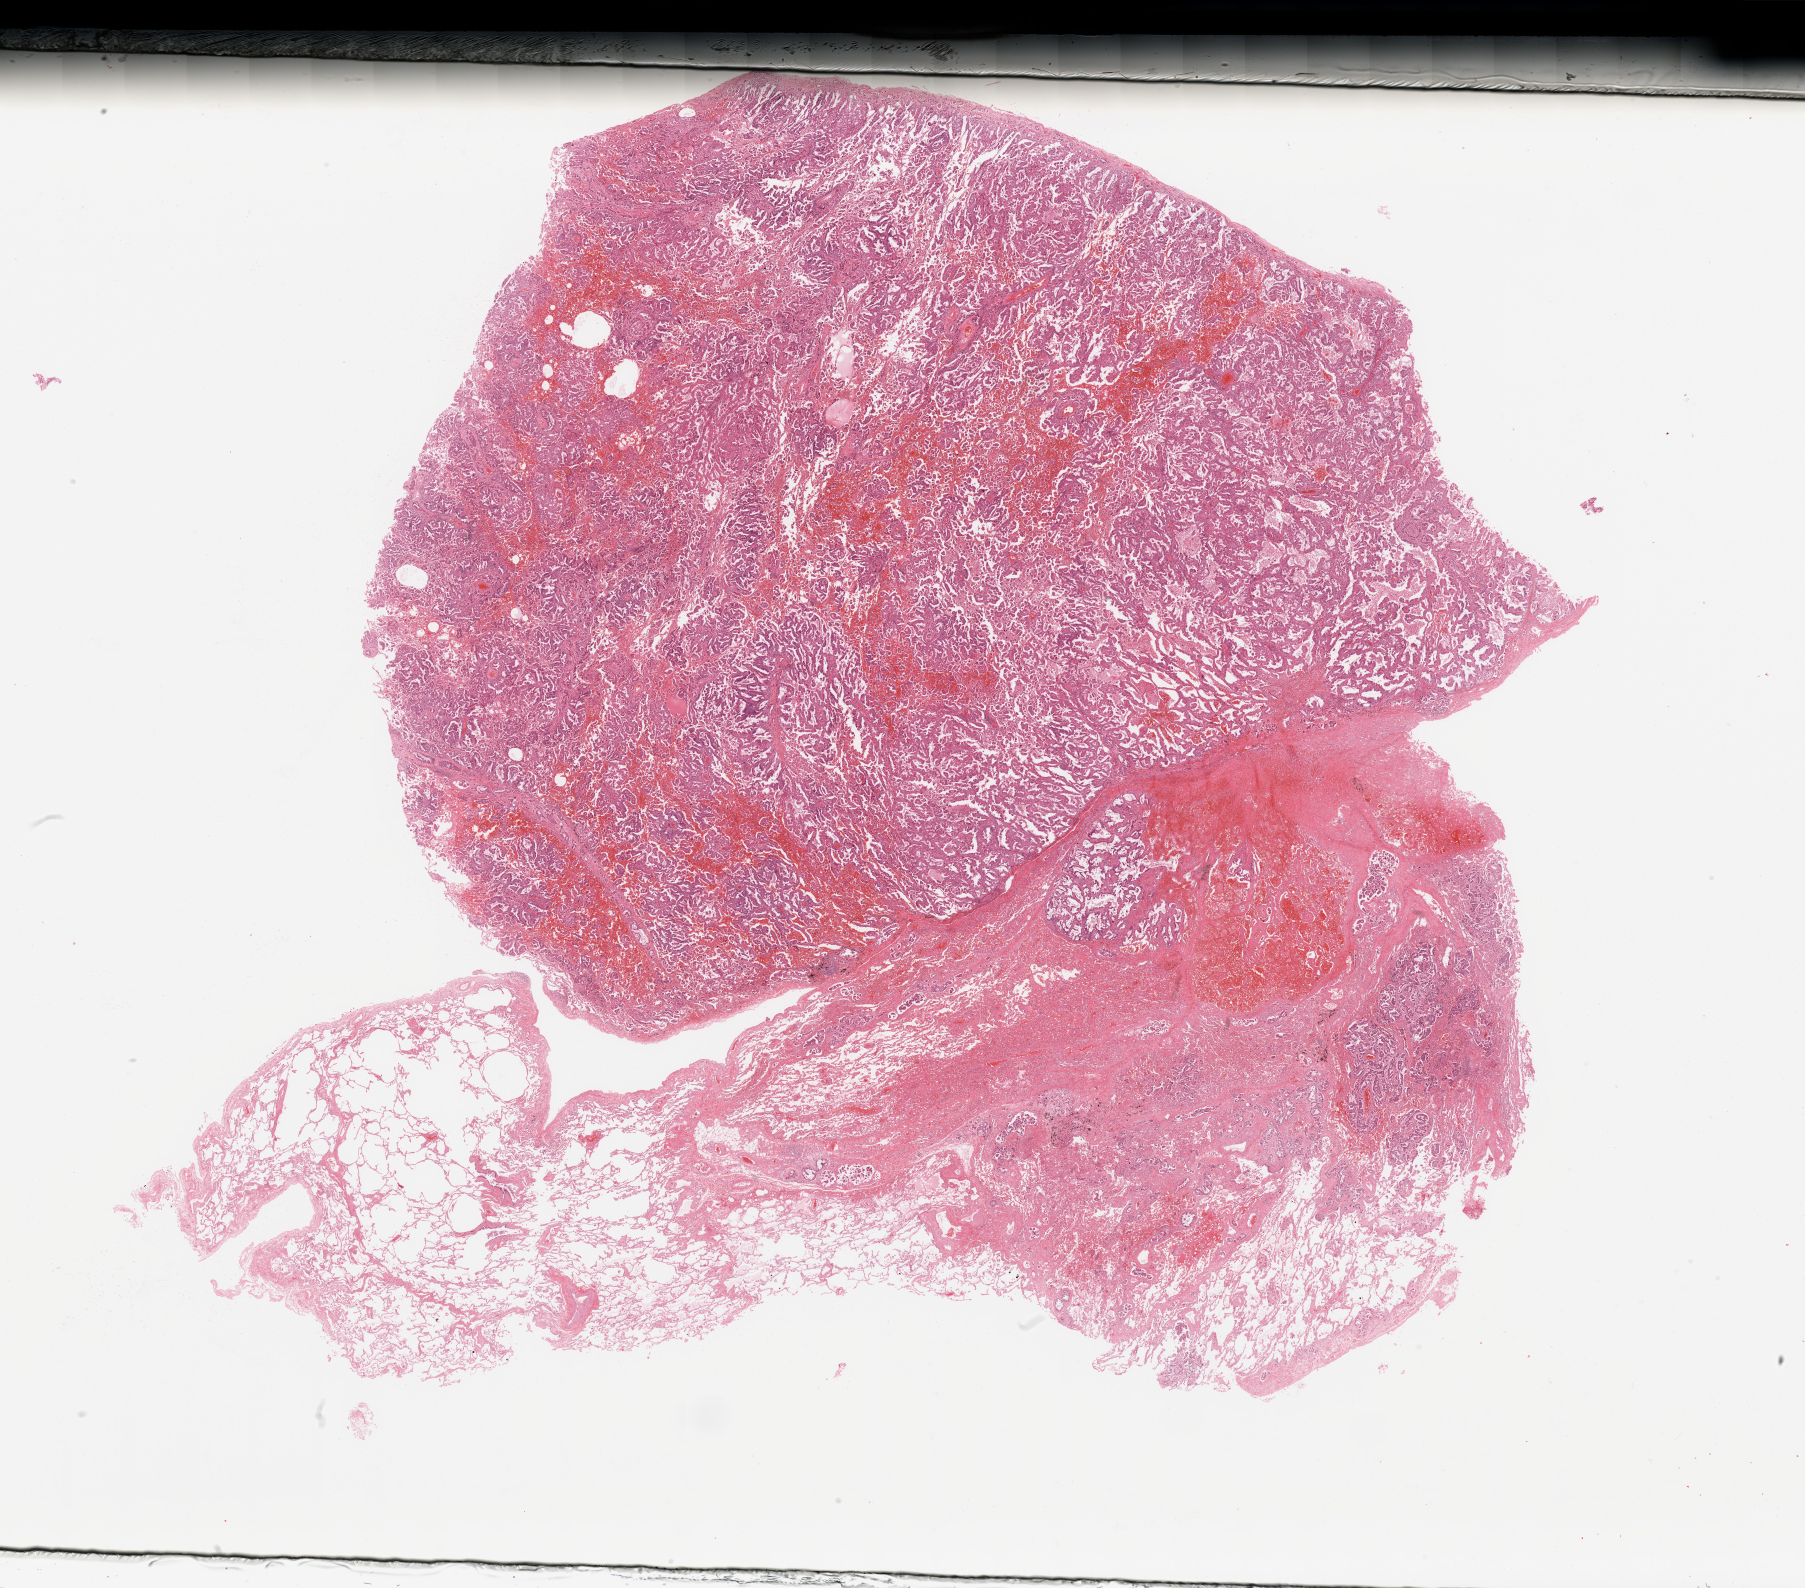
H&E-stained whole-slide image, shown as a low-resolution overview of the whole scanned area (about 28.5 x 25.1 mm); lung, tumour tissue. Male, 64 y/o. Histologic grade: G2 (moderately differentiated).
Diagnosis: Adenocarcinoma, NOS. AJCC pathologic stage: IIA.